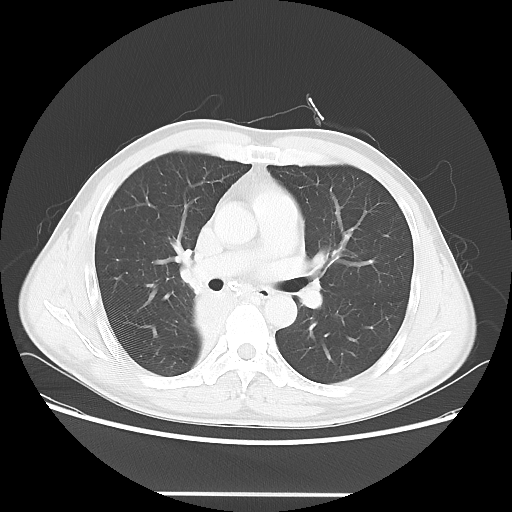
Chest CT, one axial slice; position 36 of 62 along the scan axis; reconstruction kernel LUNG; lung window (W 1500 / L -600 HU); 5 mm slice thickness; 512 × 512 image matrix, field of view 393 × 393 mm. Patient: male, 47 years. From the clinical record (not read from this slice): clinical TNM (as recorded): T2 N0 M0; histopathological grade: G2.
Outlined on this slice (rectangle marked by the reading radiologist):
- lung tumour (recorded histology: squamous cell carcinoma): bounding box <190,287,249,350> (left, top, right, bottom; pixels)